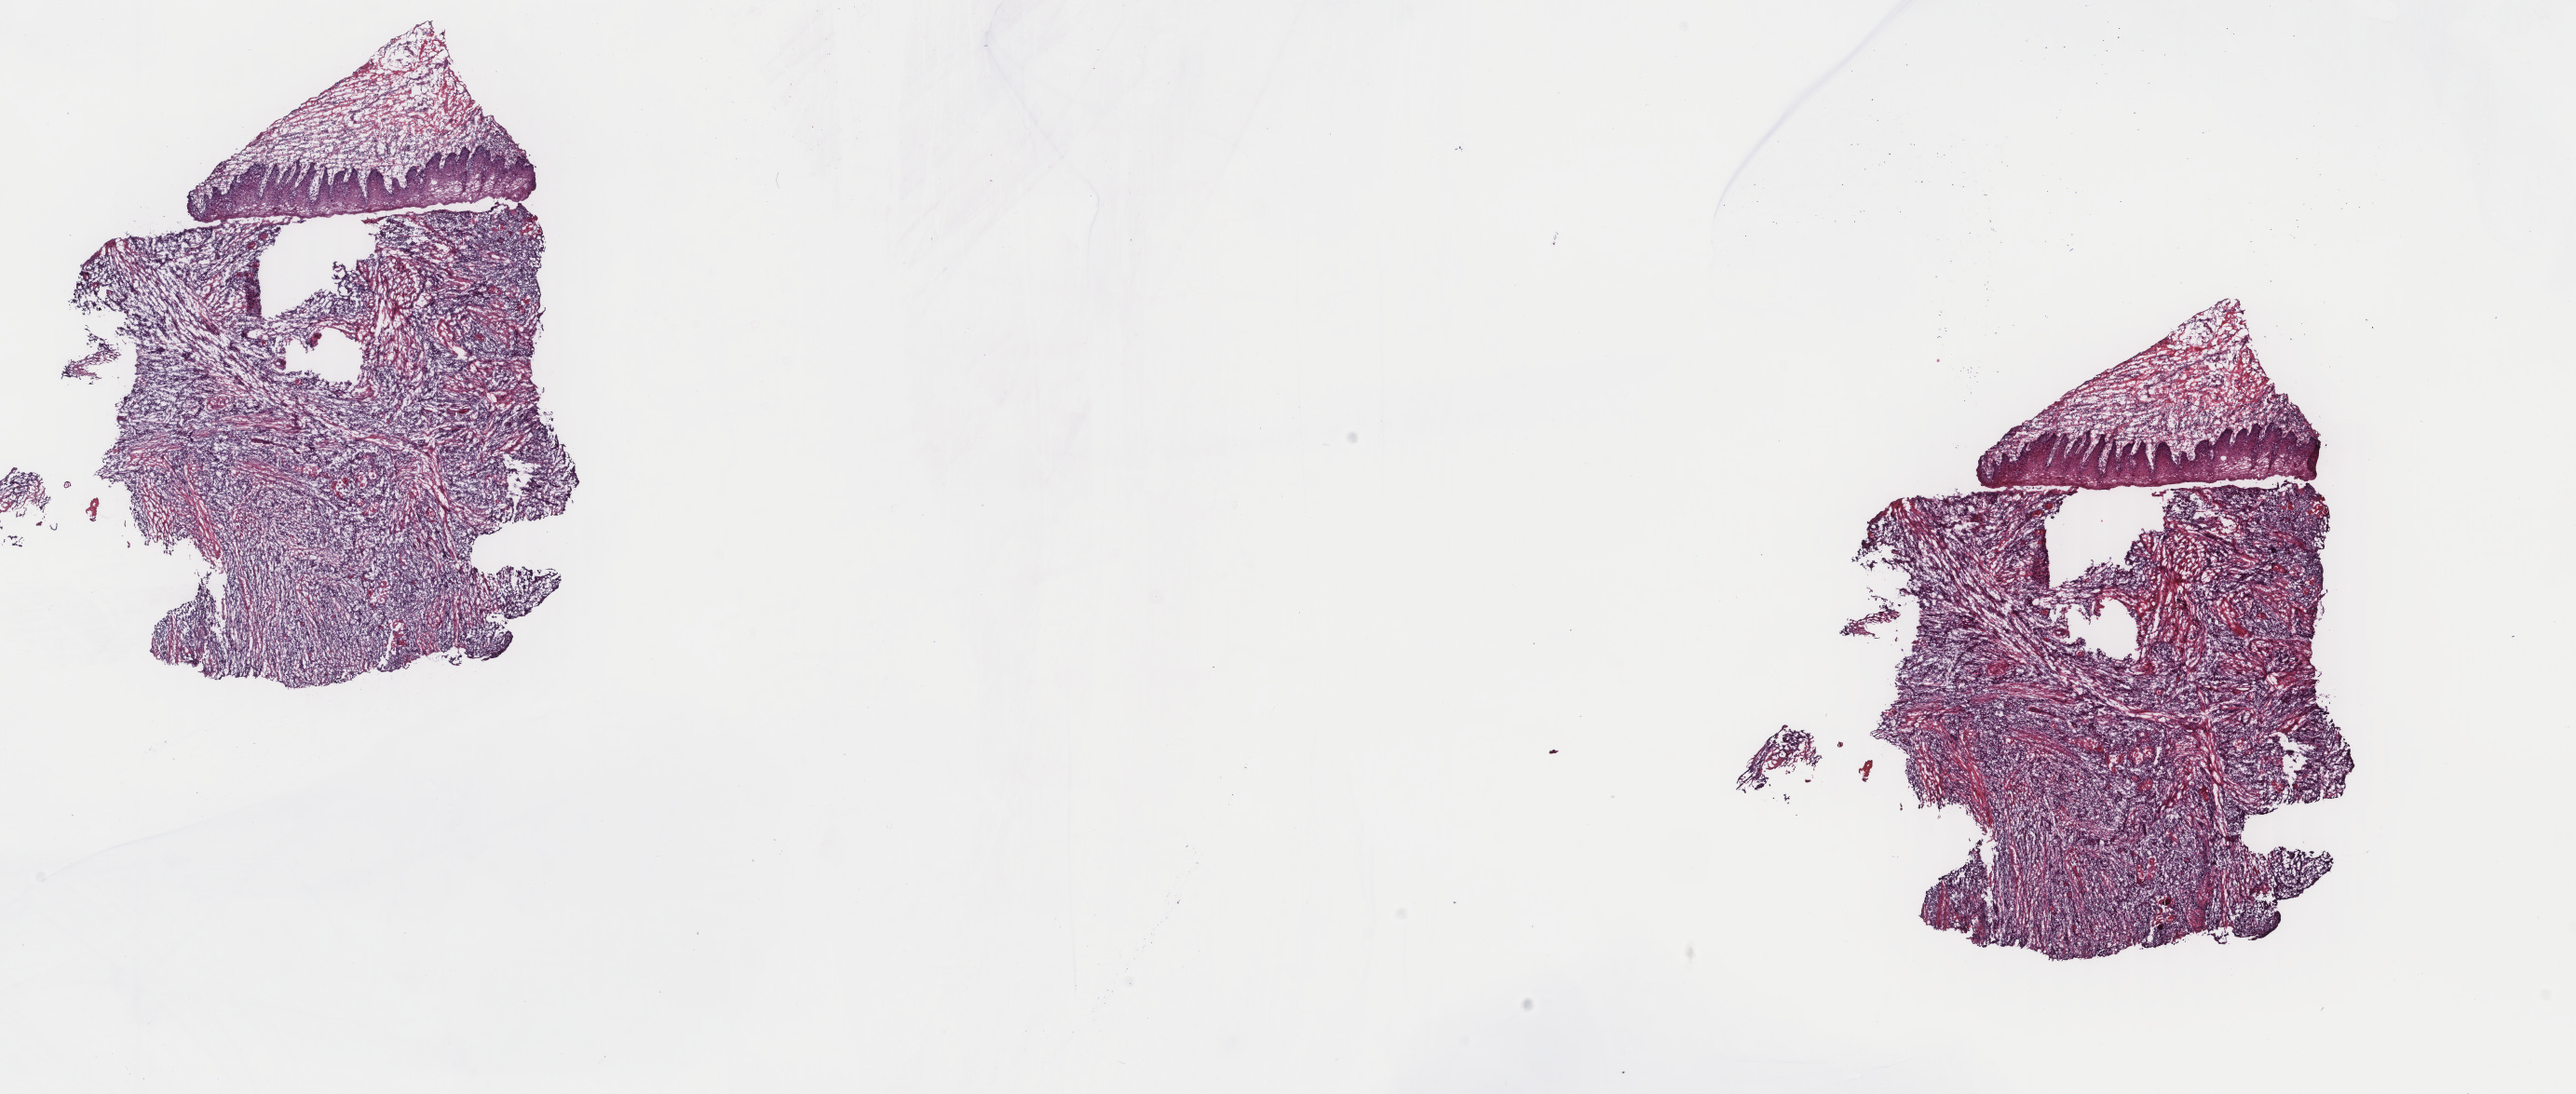
Digitized H&E tissue section (whole slide), low-resolution overview of the scanned area, about 22.0 x 9.3 mm. Frozen section from the top of the tissue portion. Primary tumour sample from the head and neck. Male, age 42 years at initial diagnosis. Histologic grade: G2 (moderately differentiated). Pathologist review of this section (percent, as recorded): tumour cells 80%, tumour nuclei 75%, normal cells 20%, stromal cells 0%, necrosis 0%. Inflammatory infiltration, as recorded: lymphocyte infiltration 3%, monocyte infiltration 0%, neutrophil infiltration 0%.
* AJCC pathologic stage: IVA (5th edition)
* histologic diagnosis: Squamous cell carcinoma, keratinizing, NOS